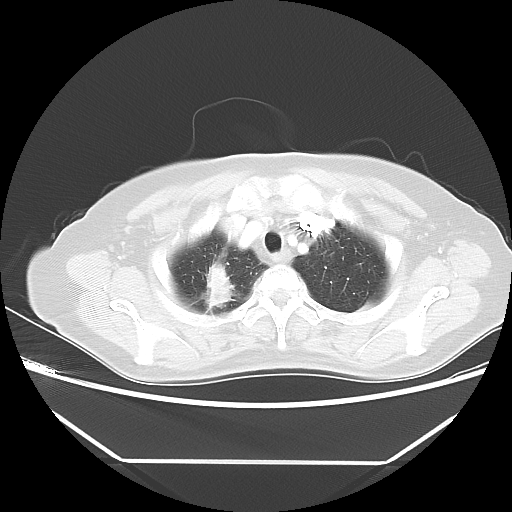
Chest CT, one axial slice; position 43 of 48 along the scan axis; reconstruction kernel LUNG; lung window (W 1500 / L -600 HU); 512 × 512 image matrix, field of view 360 × 360 mm. Patient: female, 65 years. From the clinical record (not read from this slice): clinical TNM (as recorded): T1c N1 M1.
Structures marked on this image (bounding box drawn by a radiologist):
- lung tumour (recorded histology: adenocarcinoma): box from (x=201, y=256) to (x=238, y=314) px